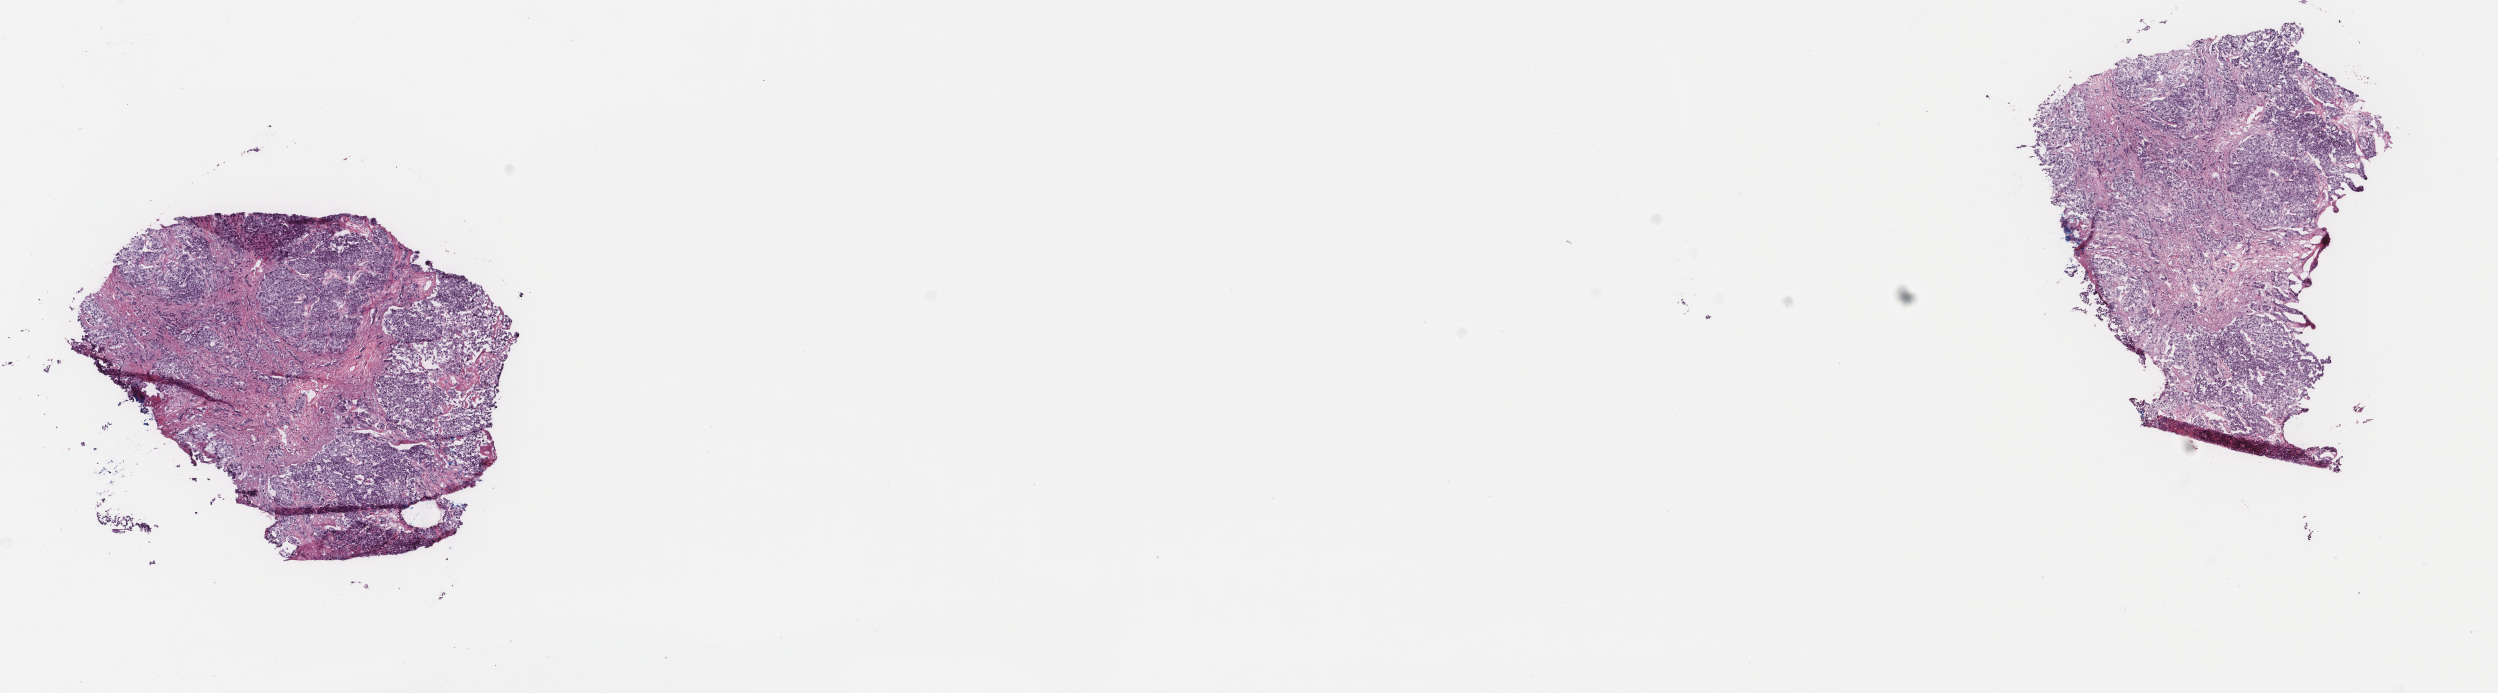
Whole-slide histology image, H&E — a low-resolution overview of the entire scanned area, about 19.8 x 5.5 mm; frozen section from the top of the tissue portion; primary tumour sample from the liver. Male, age 75 years at initial diagnosis. Histologic grade: G1 (well differentiated). Slide review estimates, as recorded: tumour cells 70%, tumour nuclei 80%, normal cells 0%, stromal cells 30%, necrosis 0%. Inflammatory infiltration, as recorded: lymphocyte infiltration 3%, monocyte infiltration 0%, neutrophil infiltration 0%.
* TNM: T1 N0 M0
* diagnosis: Hepatocellular carcinoma, NOS
* AJCC pathologic stage: I (6th edition)